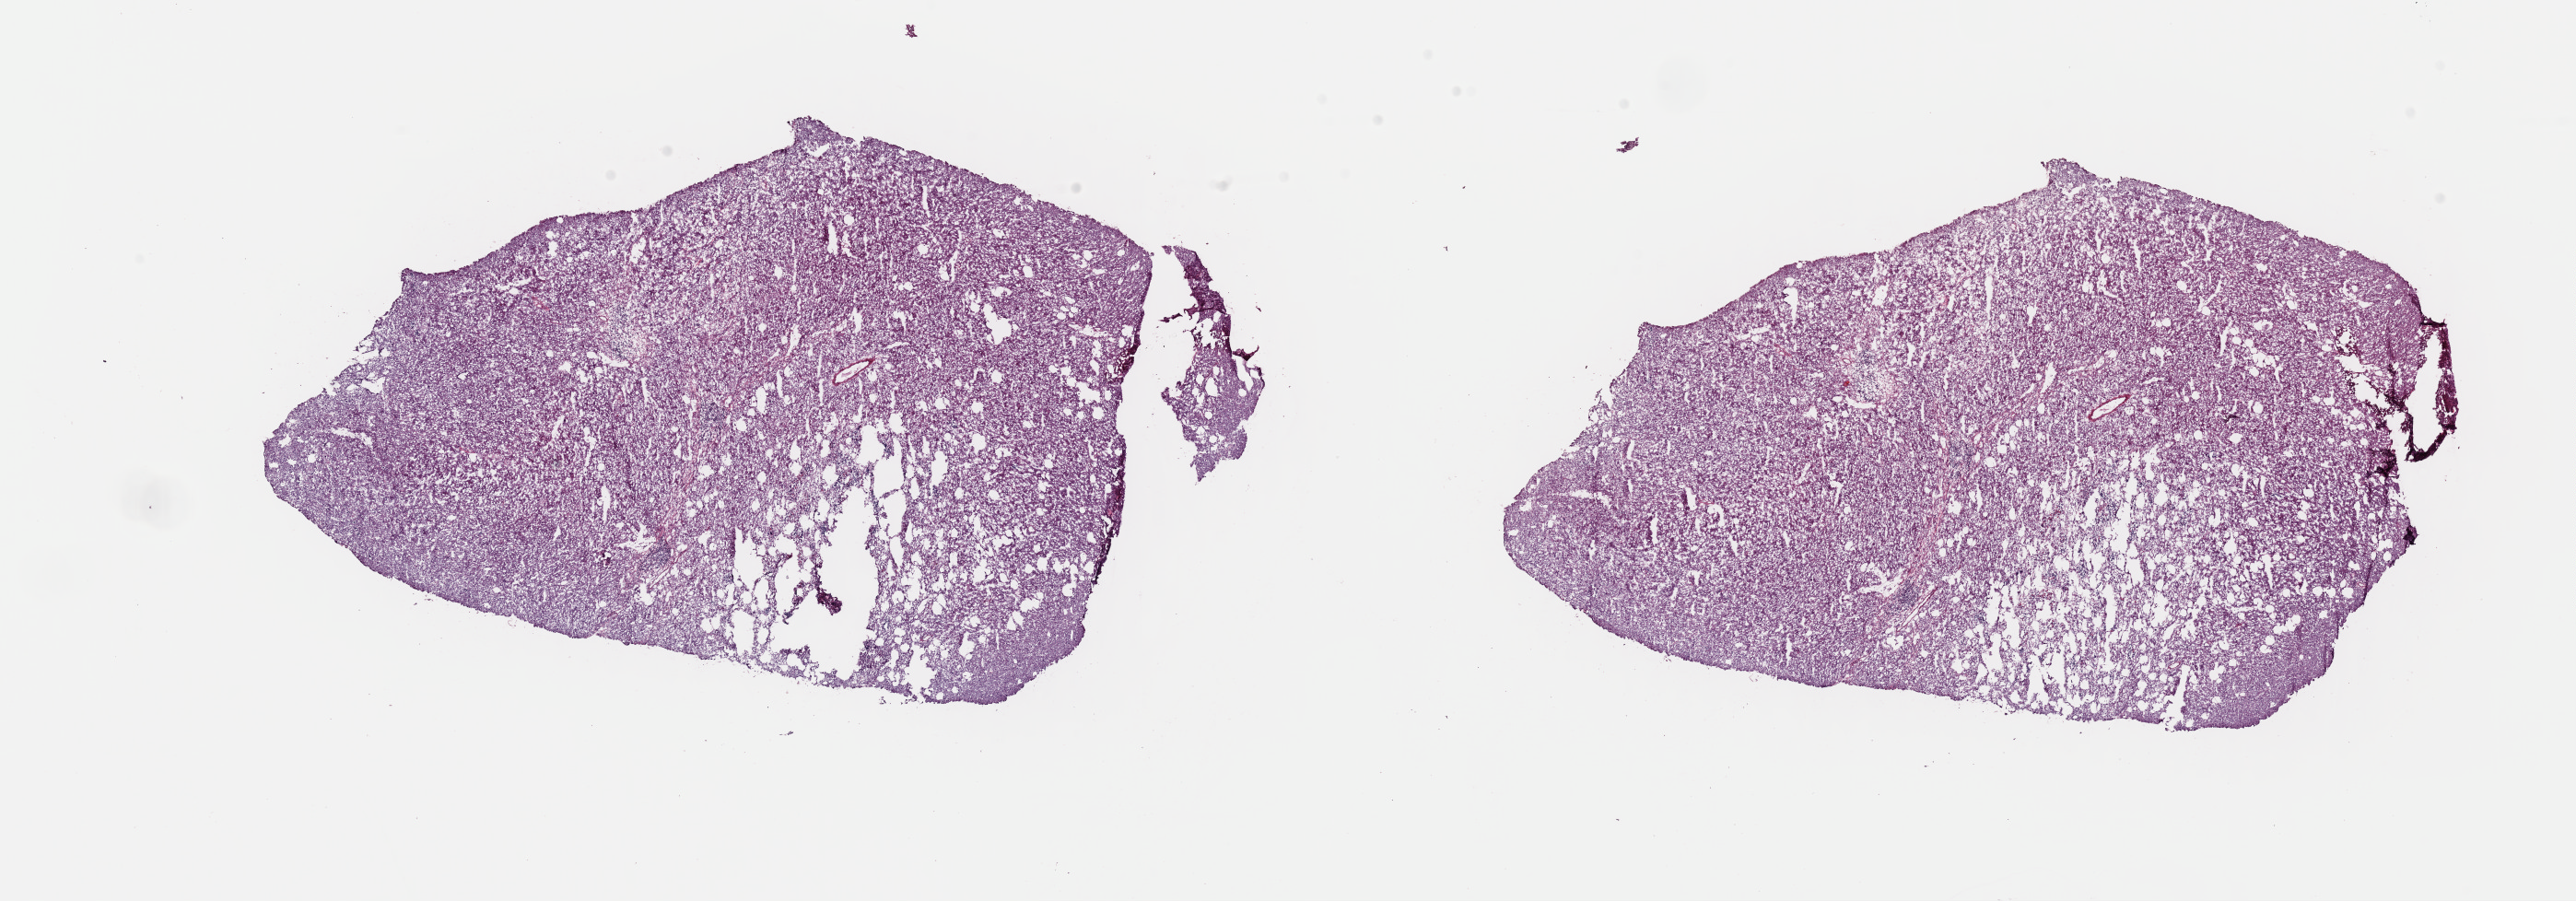
Whole-slide histology image, H&E-stained — a low-resolution overview of the entire scanned area, about 22.1 x 7.7 mm (acquisition: 40x scan). Frozen section. Liver, primary tumour sample. Male patient; age at initial diagnosis 71 years. Histologic grade: G2 (moderately differentiated). Composition of this section per pathologist review: tumour cells 100%, tumour nuclei 92%, normal cells 0%, stromal cells 0%, necrosis 0%. Inflammatory infiltration, as recorded: lymphocyte infiltration 0%, monocyte infiltration 0%, neutrophil infiltration 0%.
AJCC pathologic stage: I (7th edition). Diagnosis: Hepatocellular carcinoma, NOS.